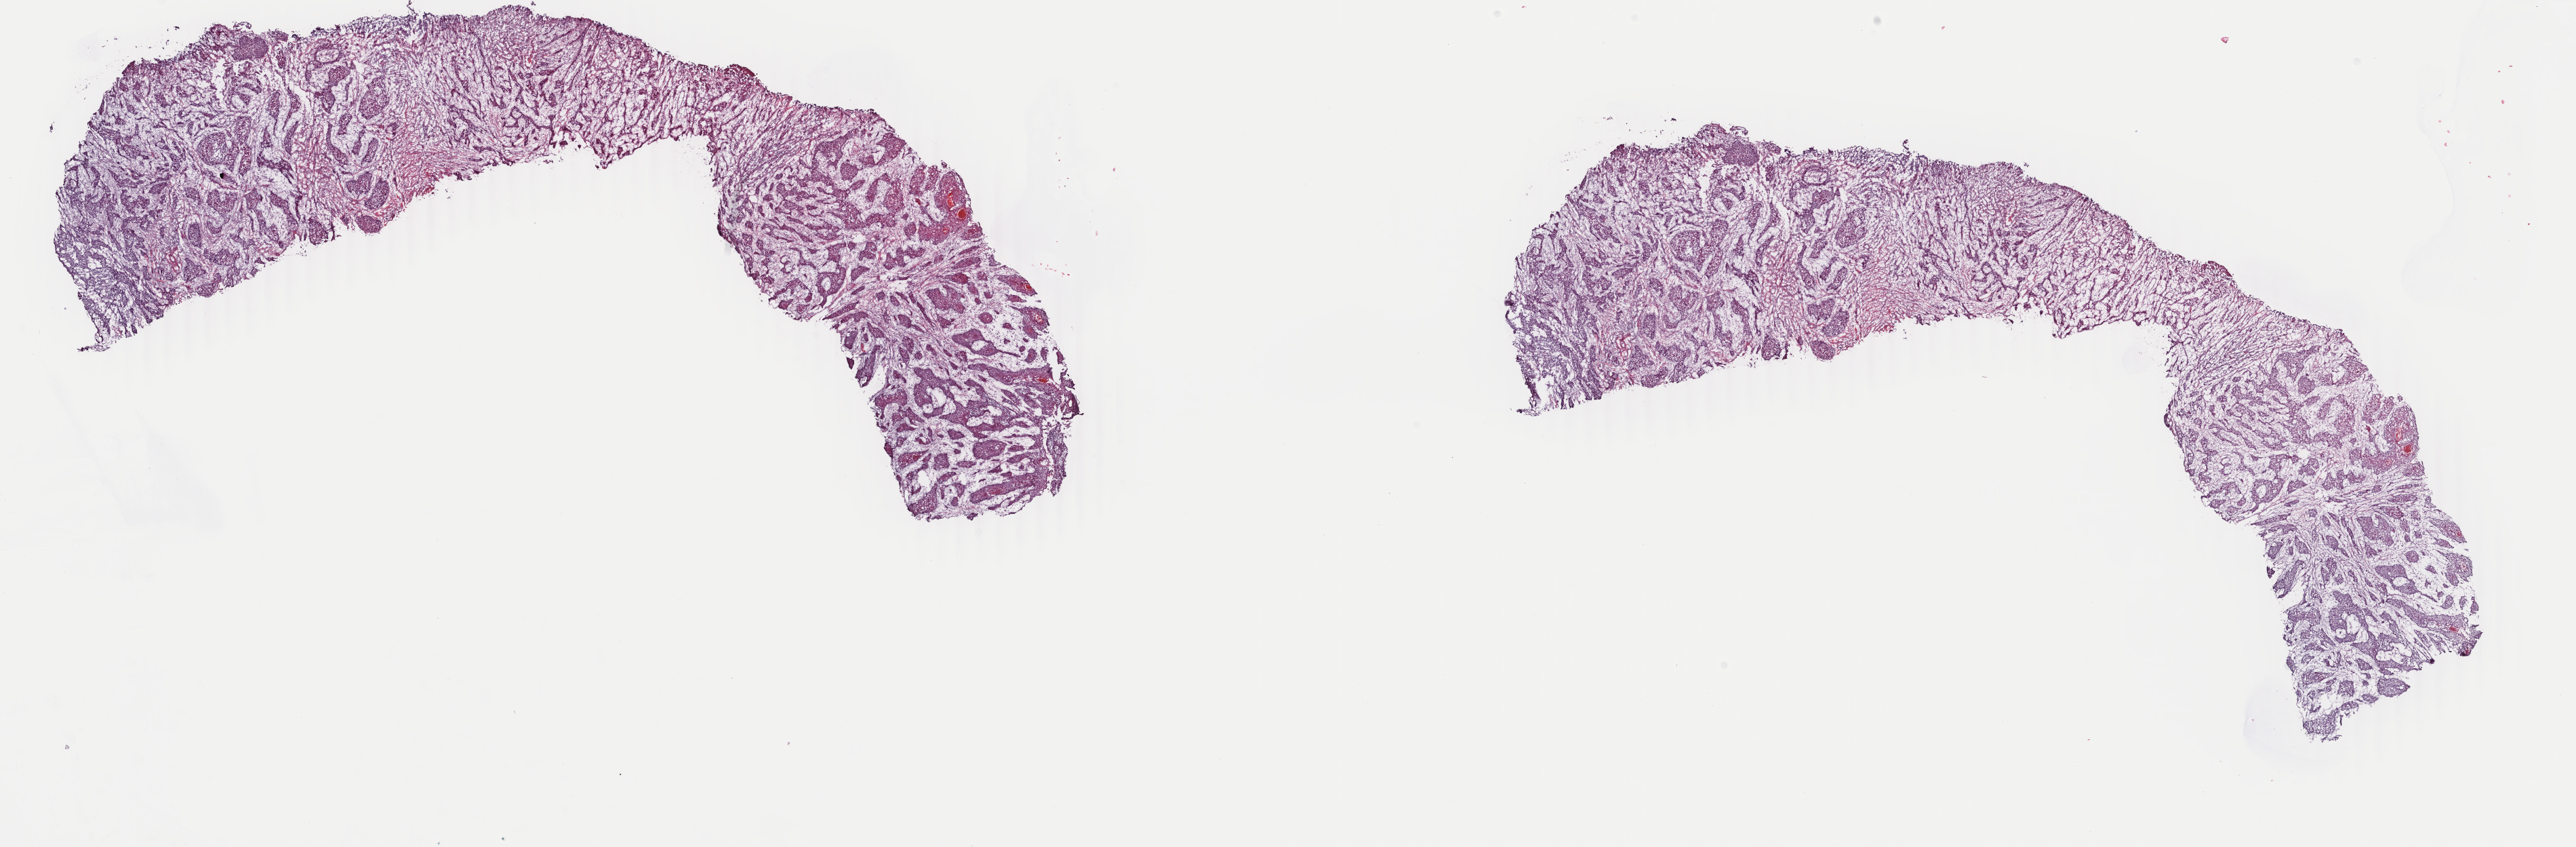
Digitized H&E-stained tissue section (whole slide), shown as a low-resolution overview of the whole scanned area (about 30.2 x 9.9 mm). Frozen section from the top of the tissue portion. Sample: primary tumour, head and neck. Female, age 79 years at initial diagnosis.
Pathologic diagnosis: Squamous cell carcinoma, NOS (floor of mouth, NOS).